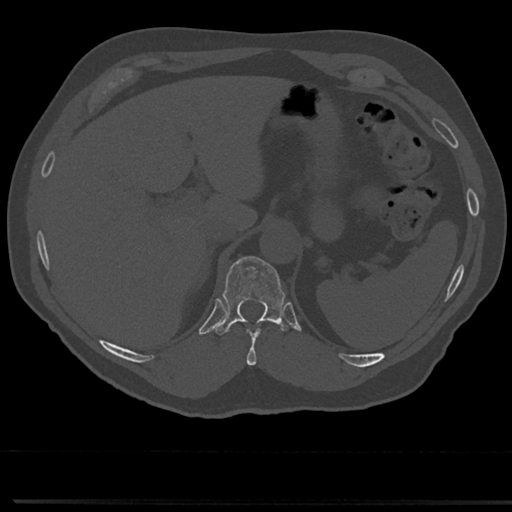
CT including the spine, one axial slice. Position 220 of 817 along the scan axis. Reconstruction kernel Br40s/3. Bone window (W 1800 / L 400 HU). 0.5 mm slice thickness. 512 × 512 image matrix. Male patient, age 61 years. From the clinical record (not read from this slice): primary cancer: prostate.
Outlined on this slice (semi-automatically segmented with operator editing):
- T10 vertebra: bounding box (x1, y1, x2, y2) in pixels: (244, 320, 275, 366)
- T11 vertebra: (219, 256, 284, 333)